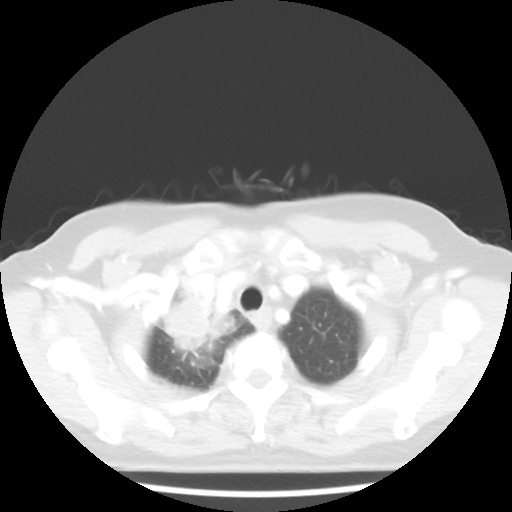
Chest CT, one axial slice; reconstruction kernel STANDARD; 100 kVp; lung window (W 1500 / L -600 HU); 5 mm slice thickness; 512 × 512 image matrix, field of view 316 × 316 mm. Female patient, age 62 years. From the clinical record (not read from this slice): clinical TNM (as recorded): T3 N0 M0; histopathological grade: G3.
Structures marked on this image (bounding box drawn by a radiologist):
- lung tumour (recorded histology: small cell carcinoma): bounding box (x1, y1, x2, y2) in pixels: (157, 289, 235, 358)